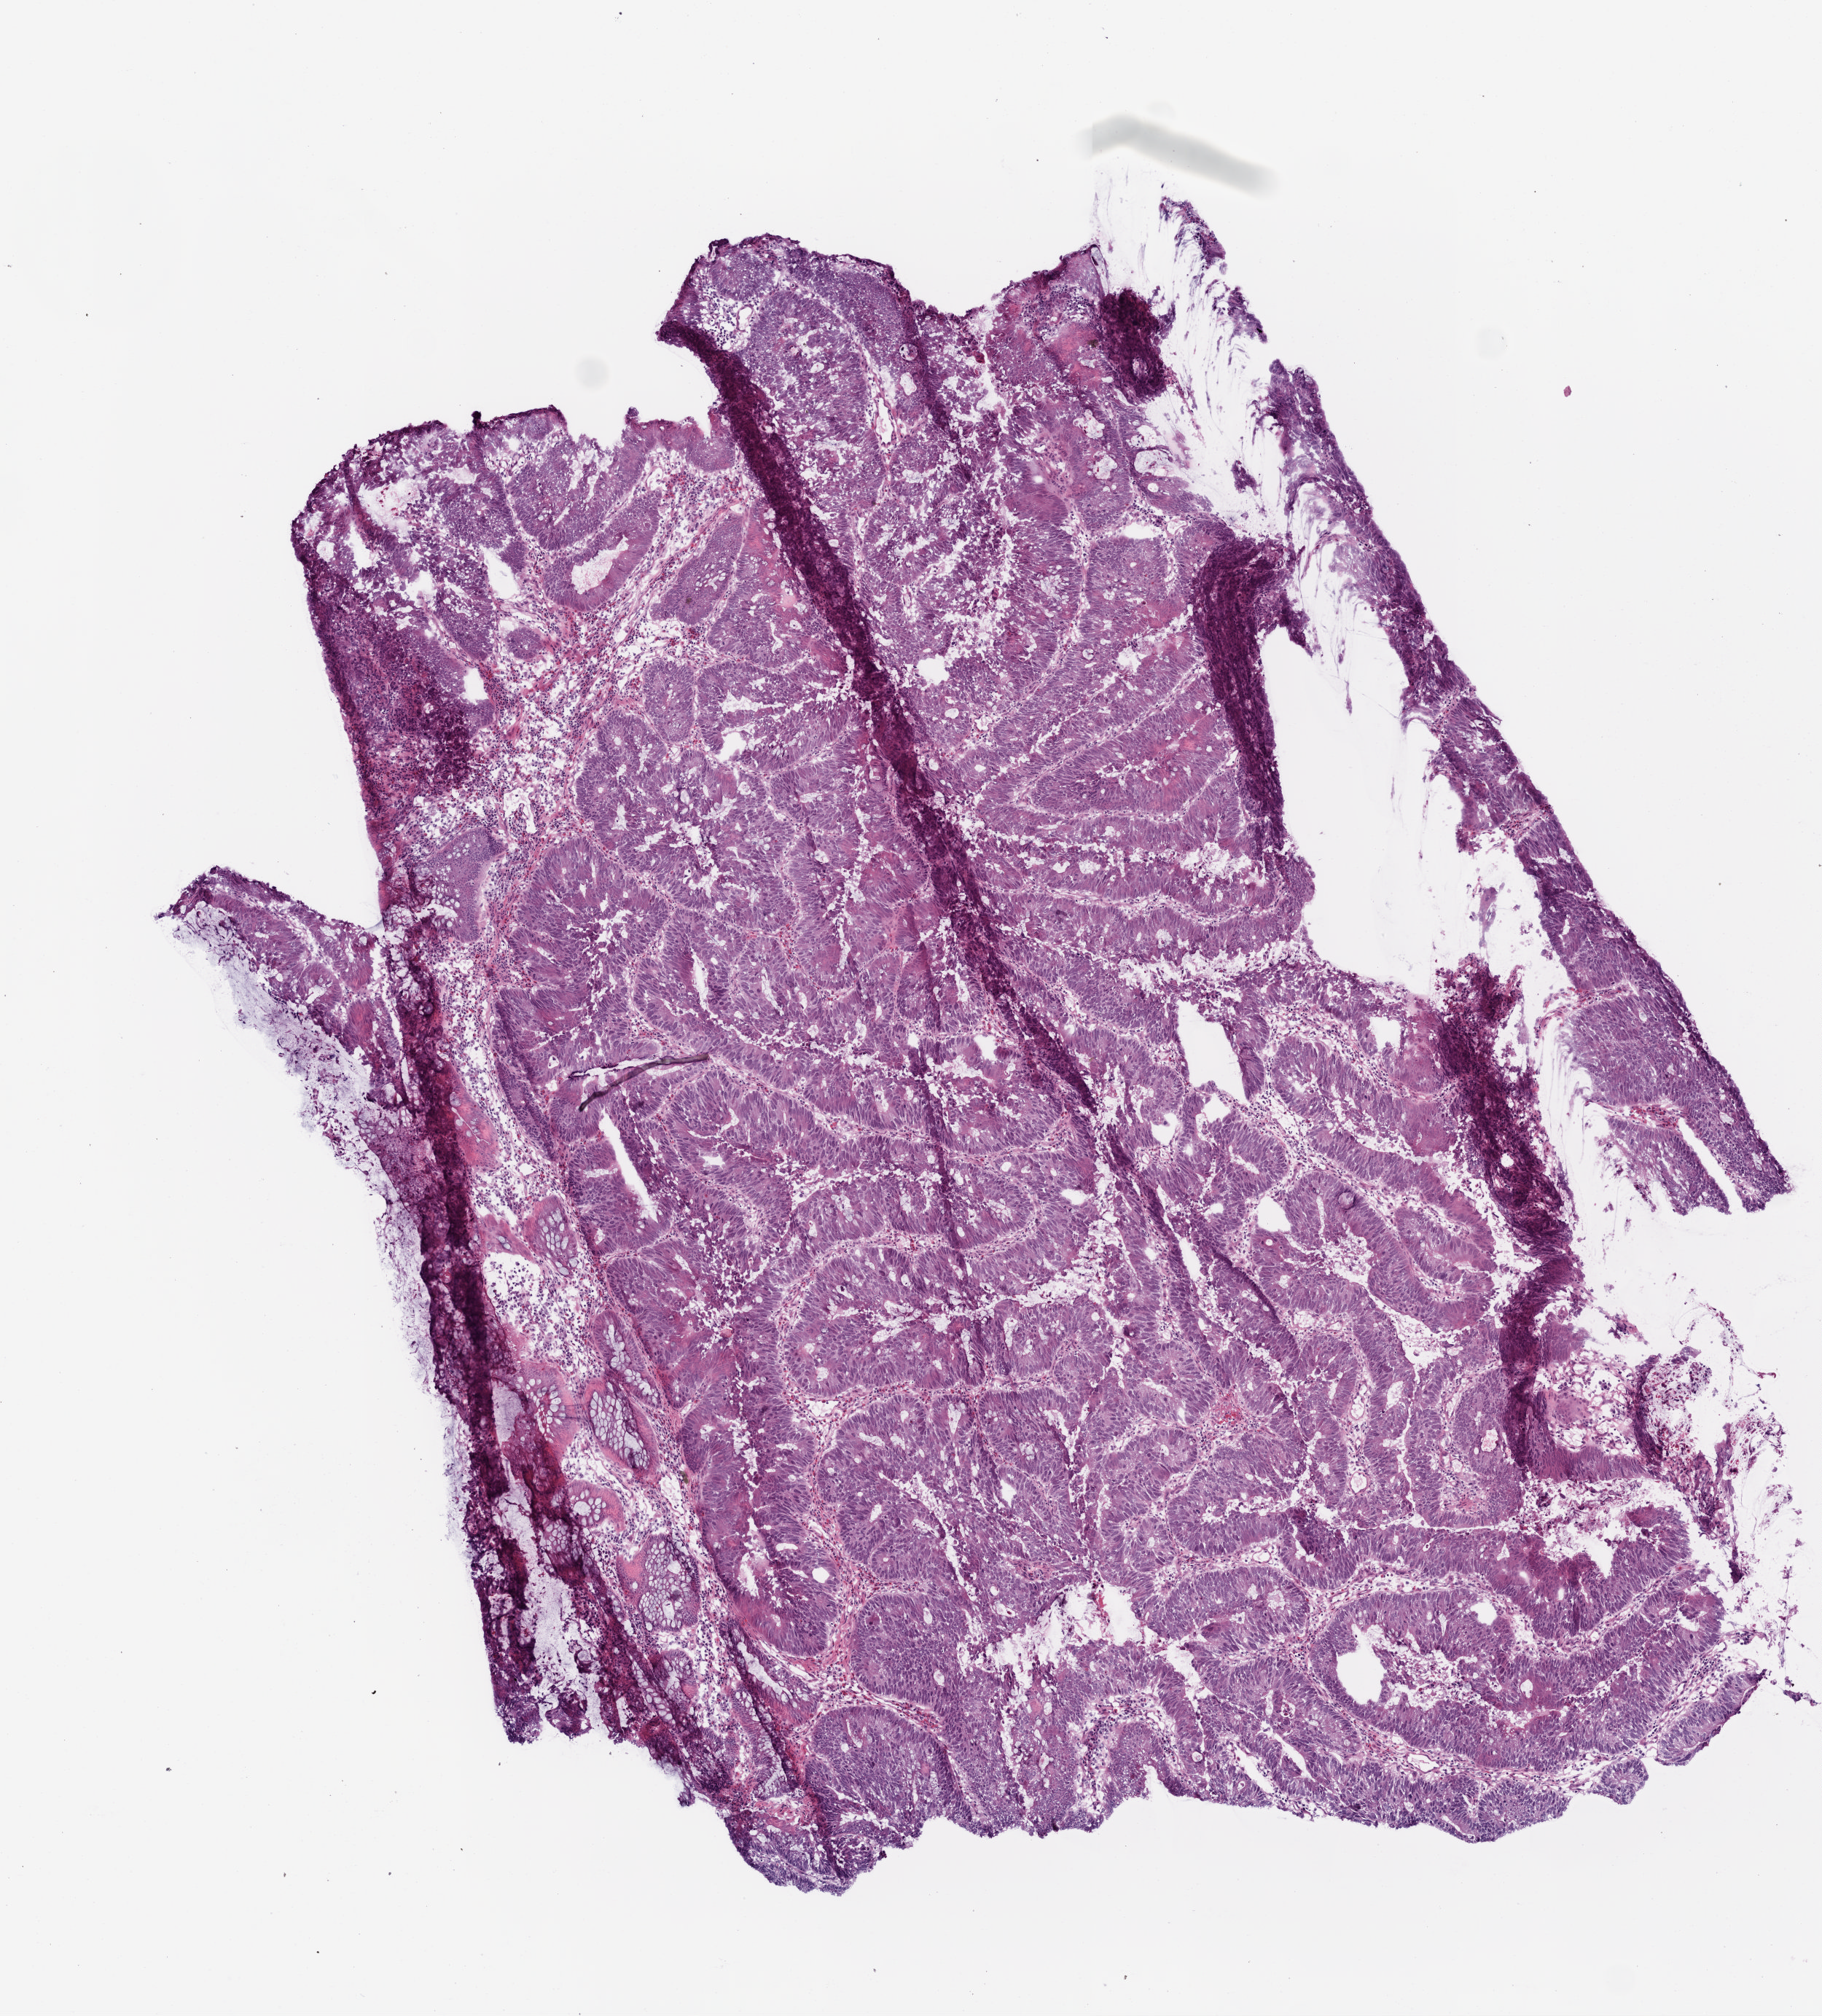
Digitized H&E tissue section (whole slide) — whole scanned area (about 5.0 x 5.5 mm, from a 20x scan) shown as a low-resolution overview, frozen section, primary tumour sample from the rectum. Patient: male, age at initial diagnosis 66 years. Slide review estimates, as recorded: tumour cells 80%, tumour nuclei 75%, normal cells 5%, stromal cells 7%, necrosis 8%.
AJCC pathologic stage: IV. Diagnosis: Adenocarcinoma, NOS (rectosigmoid junction). Lymph nodes positive (case pathology): 9 of 34 examined.